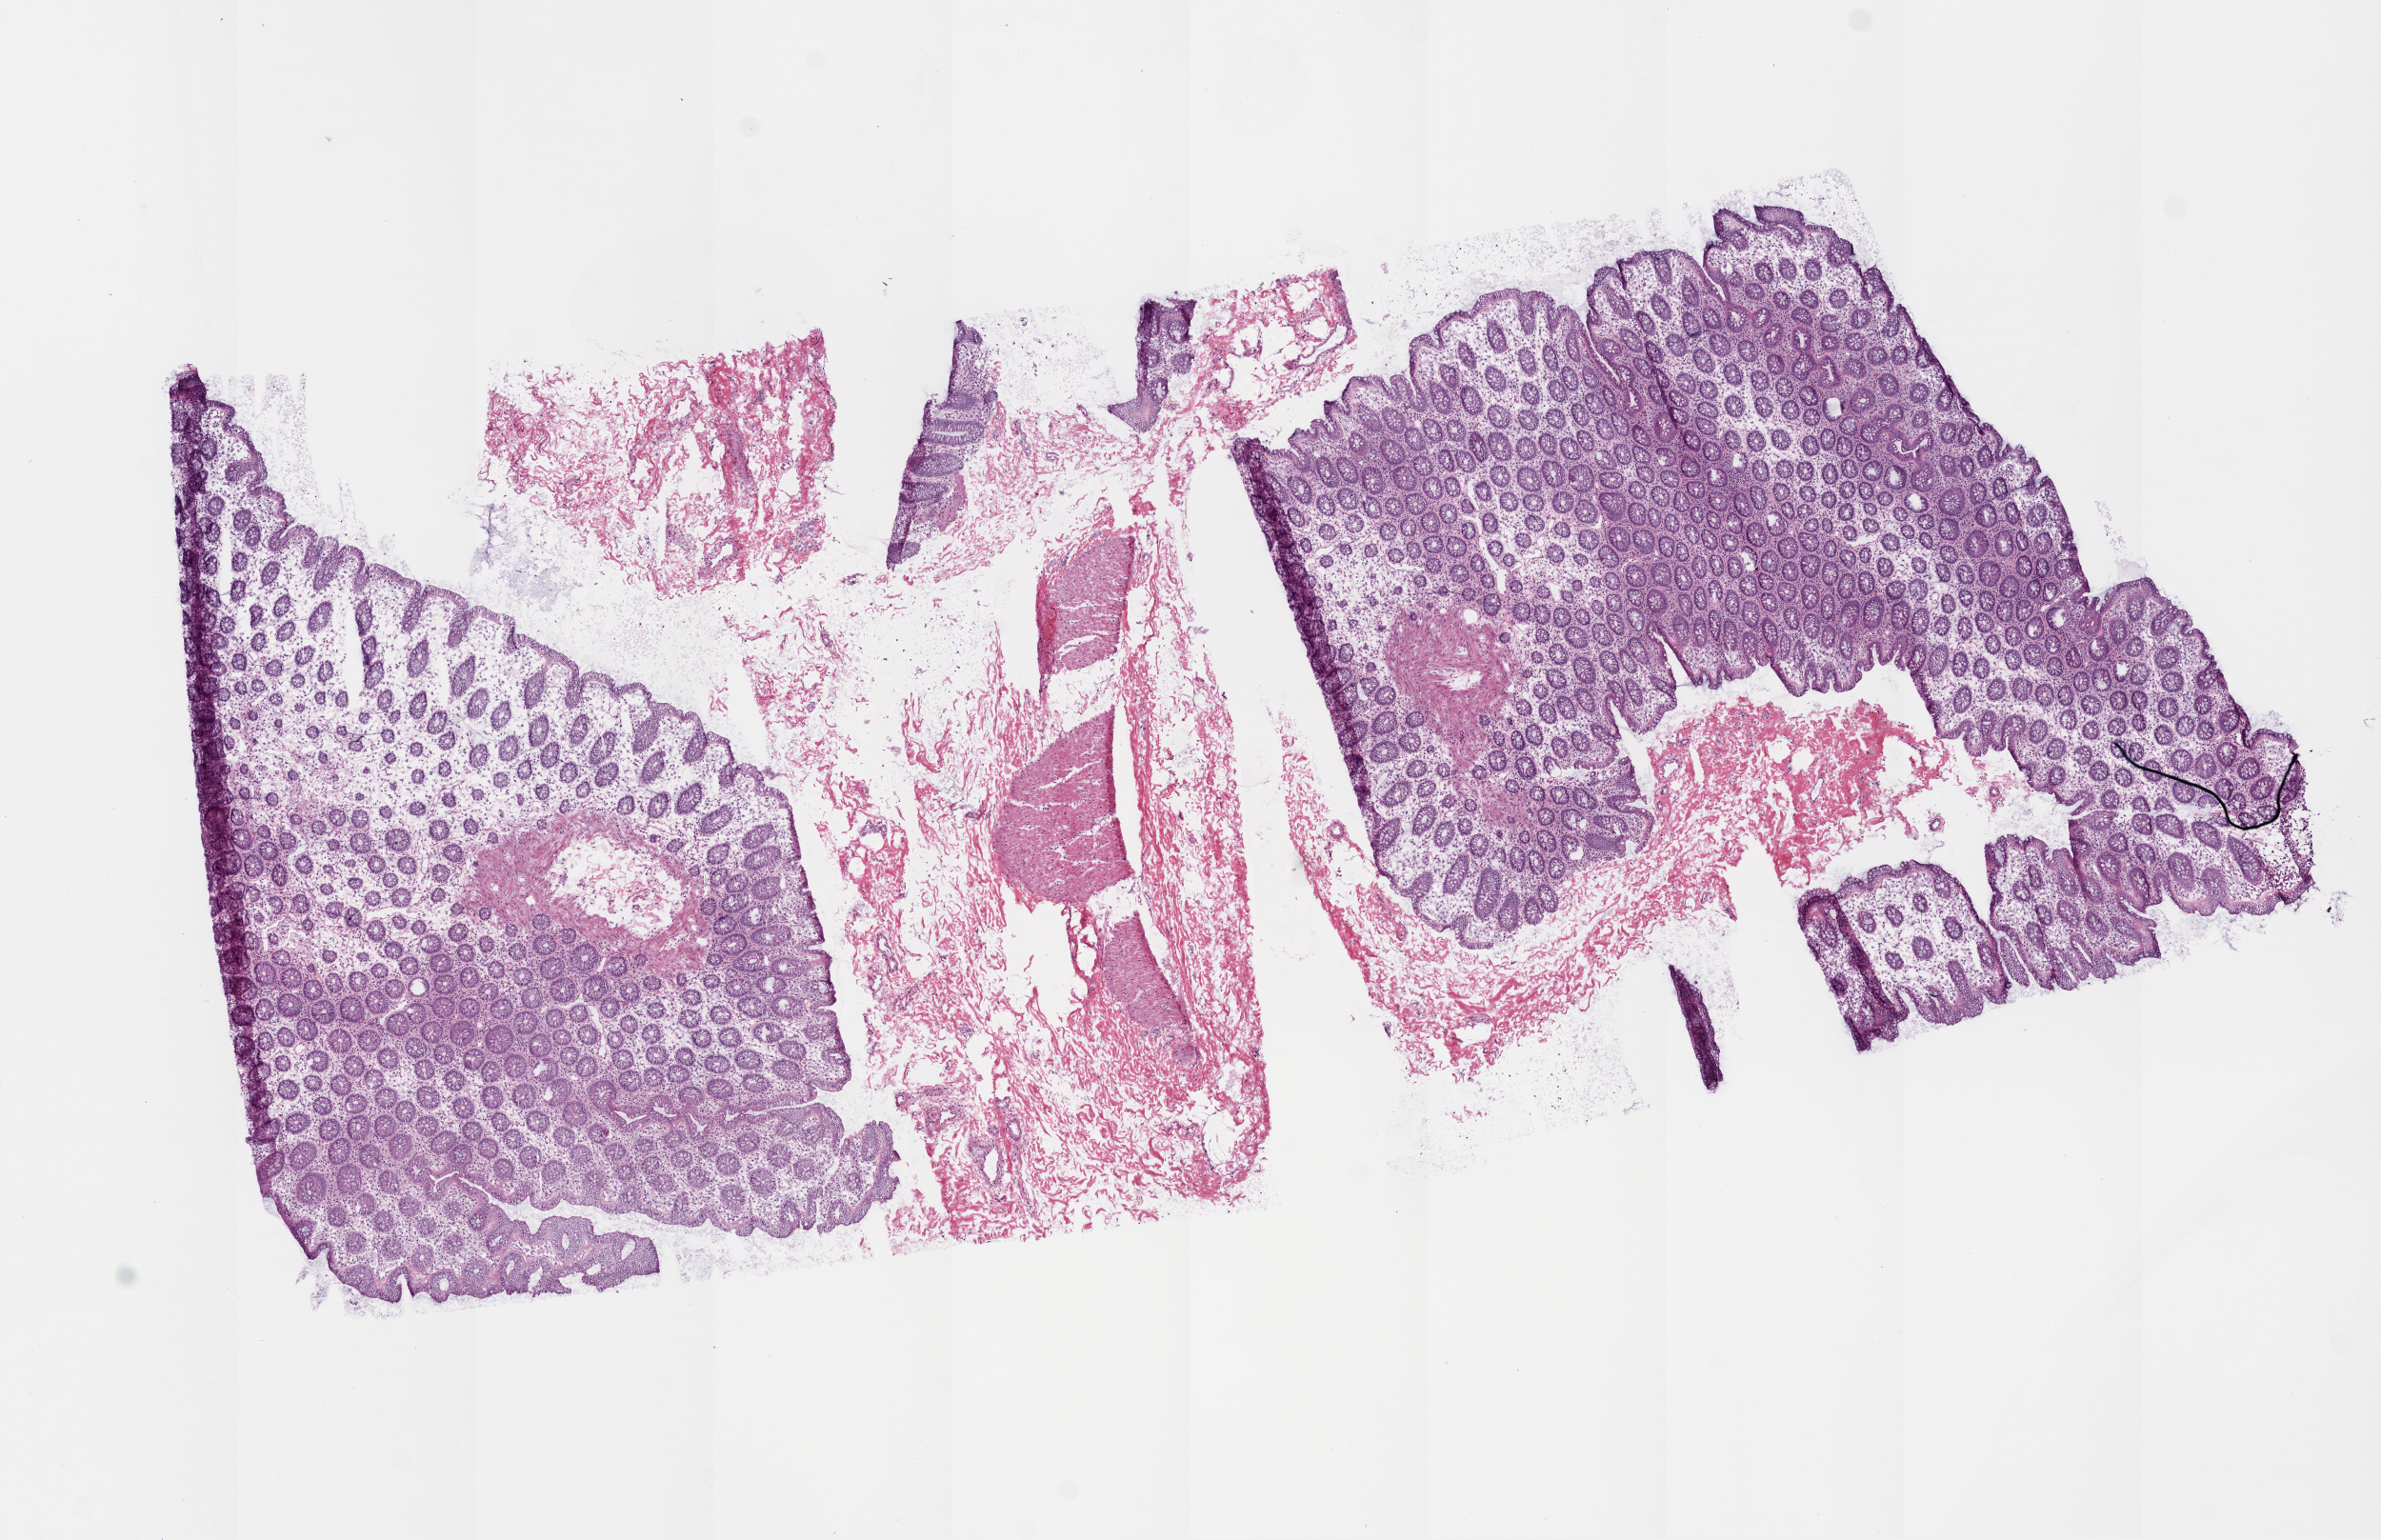
H&E-stained whole-slide image, low-resolution overview of the scanned area, about 10.0 x 6.5 mm. Frozen section from the top of the tissue portion. Sample: solid tissue normal (non-tumour tissue), colon. Female patient; age at initial diagnosis 43 years.
This section: solid tissue normal sample (biorepository sample class). Patient diagnosis: Adenocarcinoma, NOS (transverse colon).